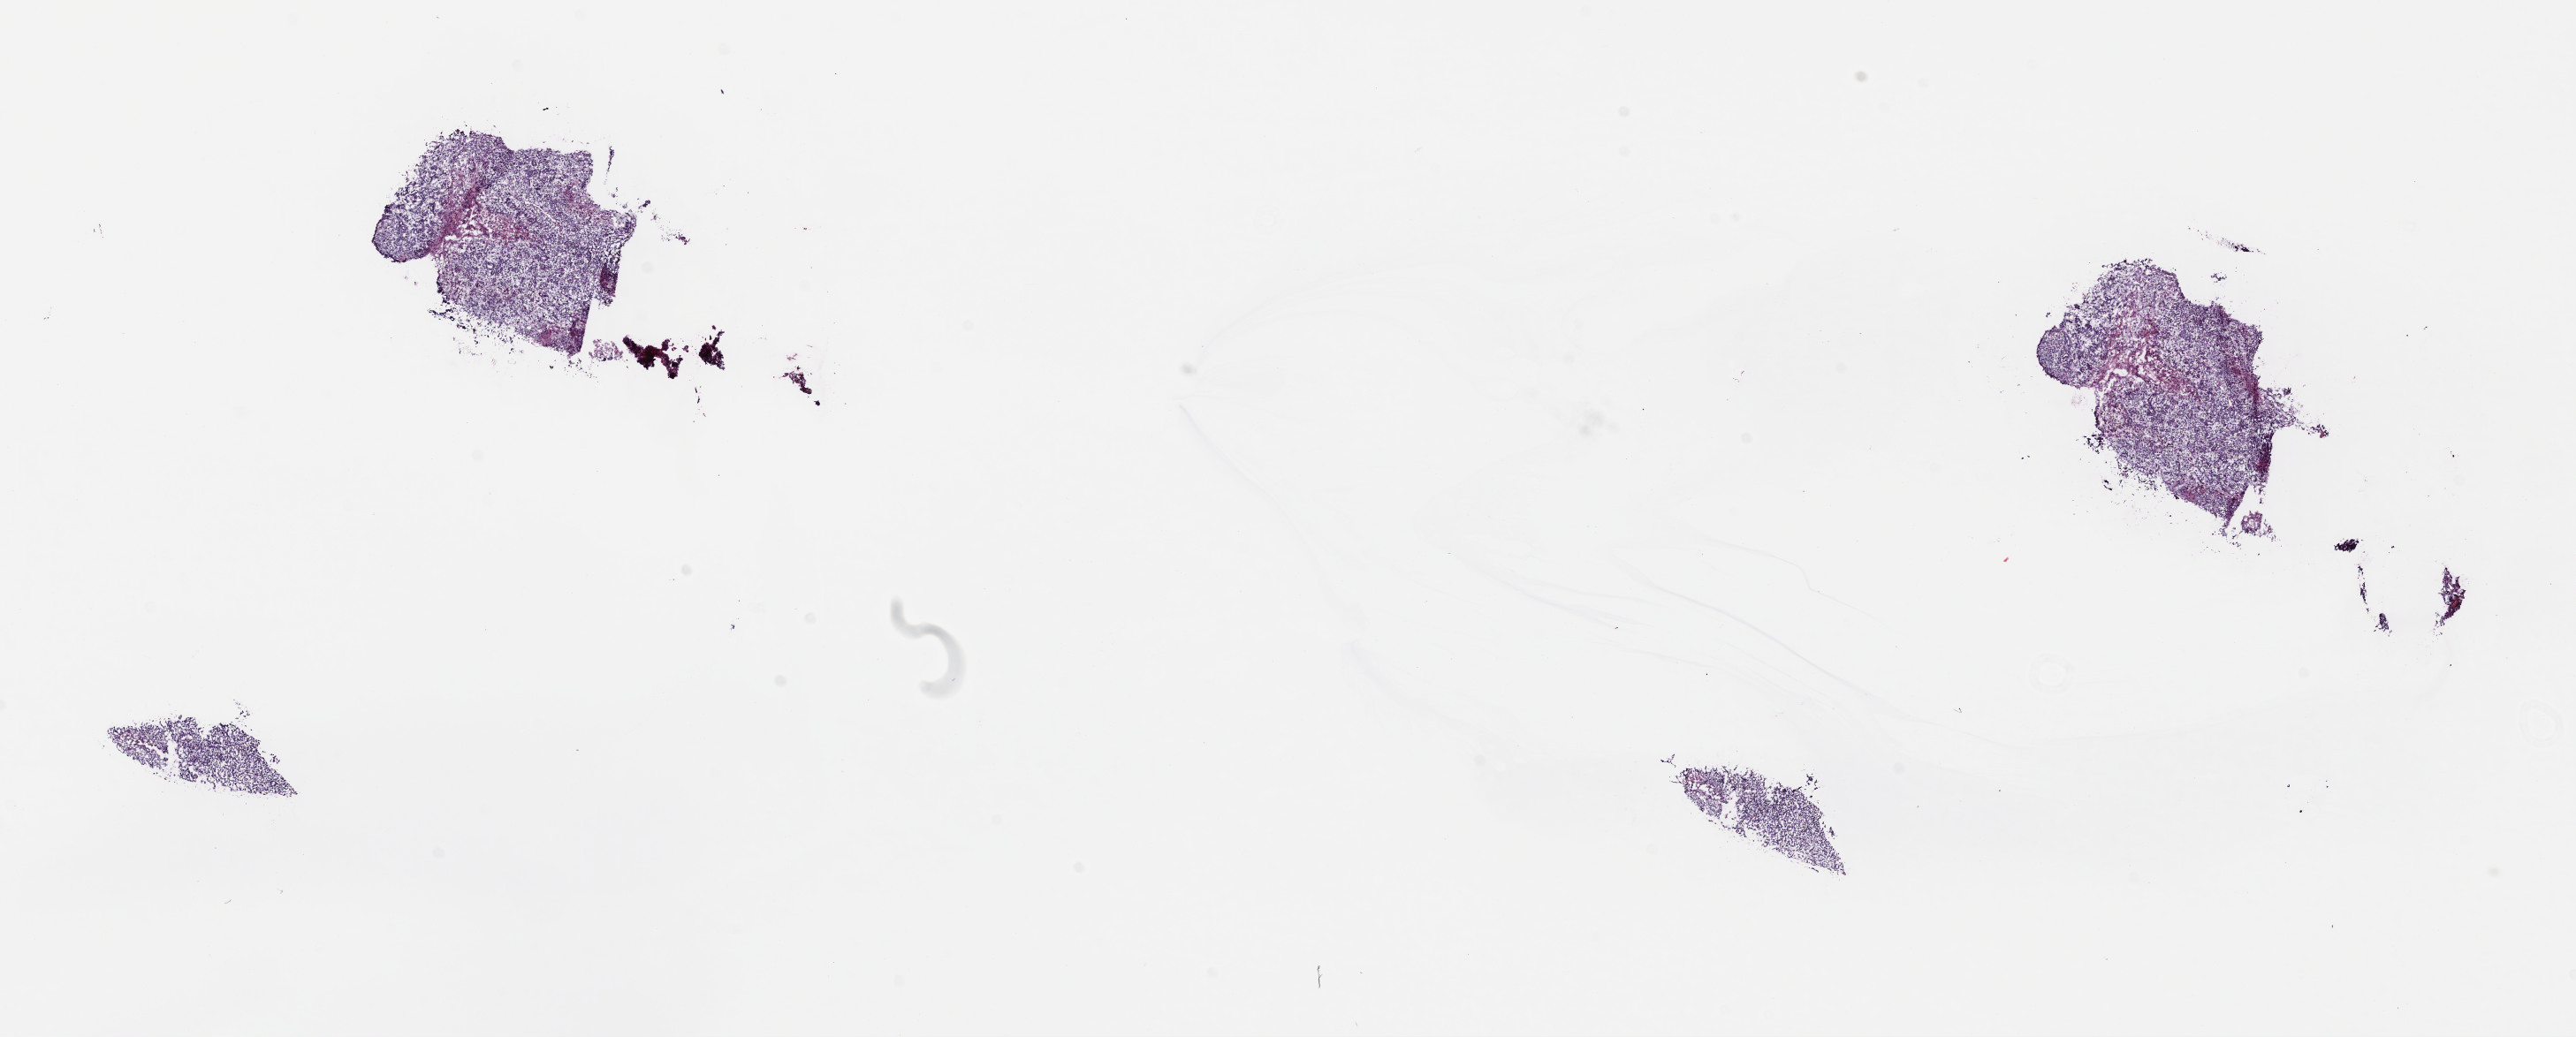
Digitized H&E tissue section (whole slide), shown as a low-resolution overview of the whole scanned area (about 22.9 x 9.2 mm), frozen section from the top of the tissue portion, uterus, primary tumour sample. Patient: female, age at initial diagnosis 82 years. Slide review estimates, as recorded: tumour cells 93%, tumour nuclei 85%, normal cells 0%, stromal cells 0%, necrosis 7%. Inflammatory infiltration, as recorded: lymphocyte infiltration 1%, monocyte infiltration 0%, neutrophil infiltration 0%.
Lymph nodes positive (case pathology): 0 of 7 examined. FIGO stage: IA. Diagnosis: Mullerian mixed tumor.